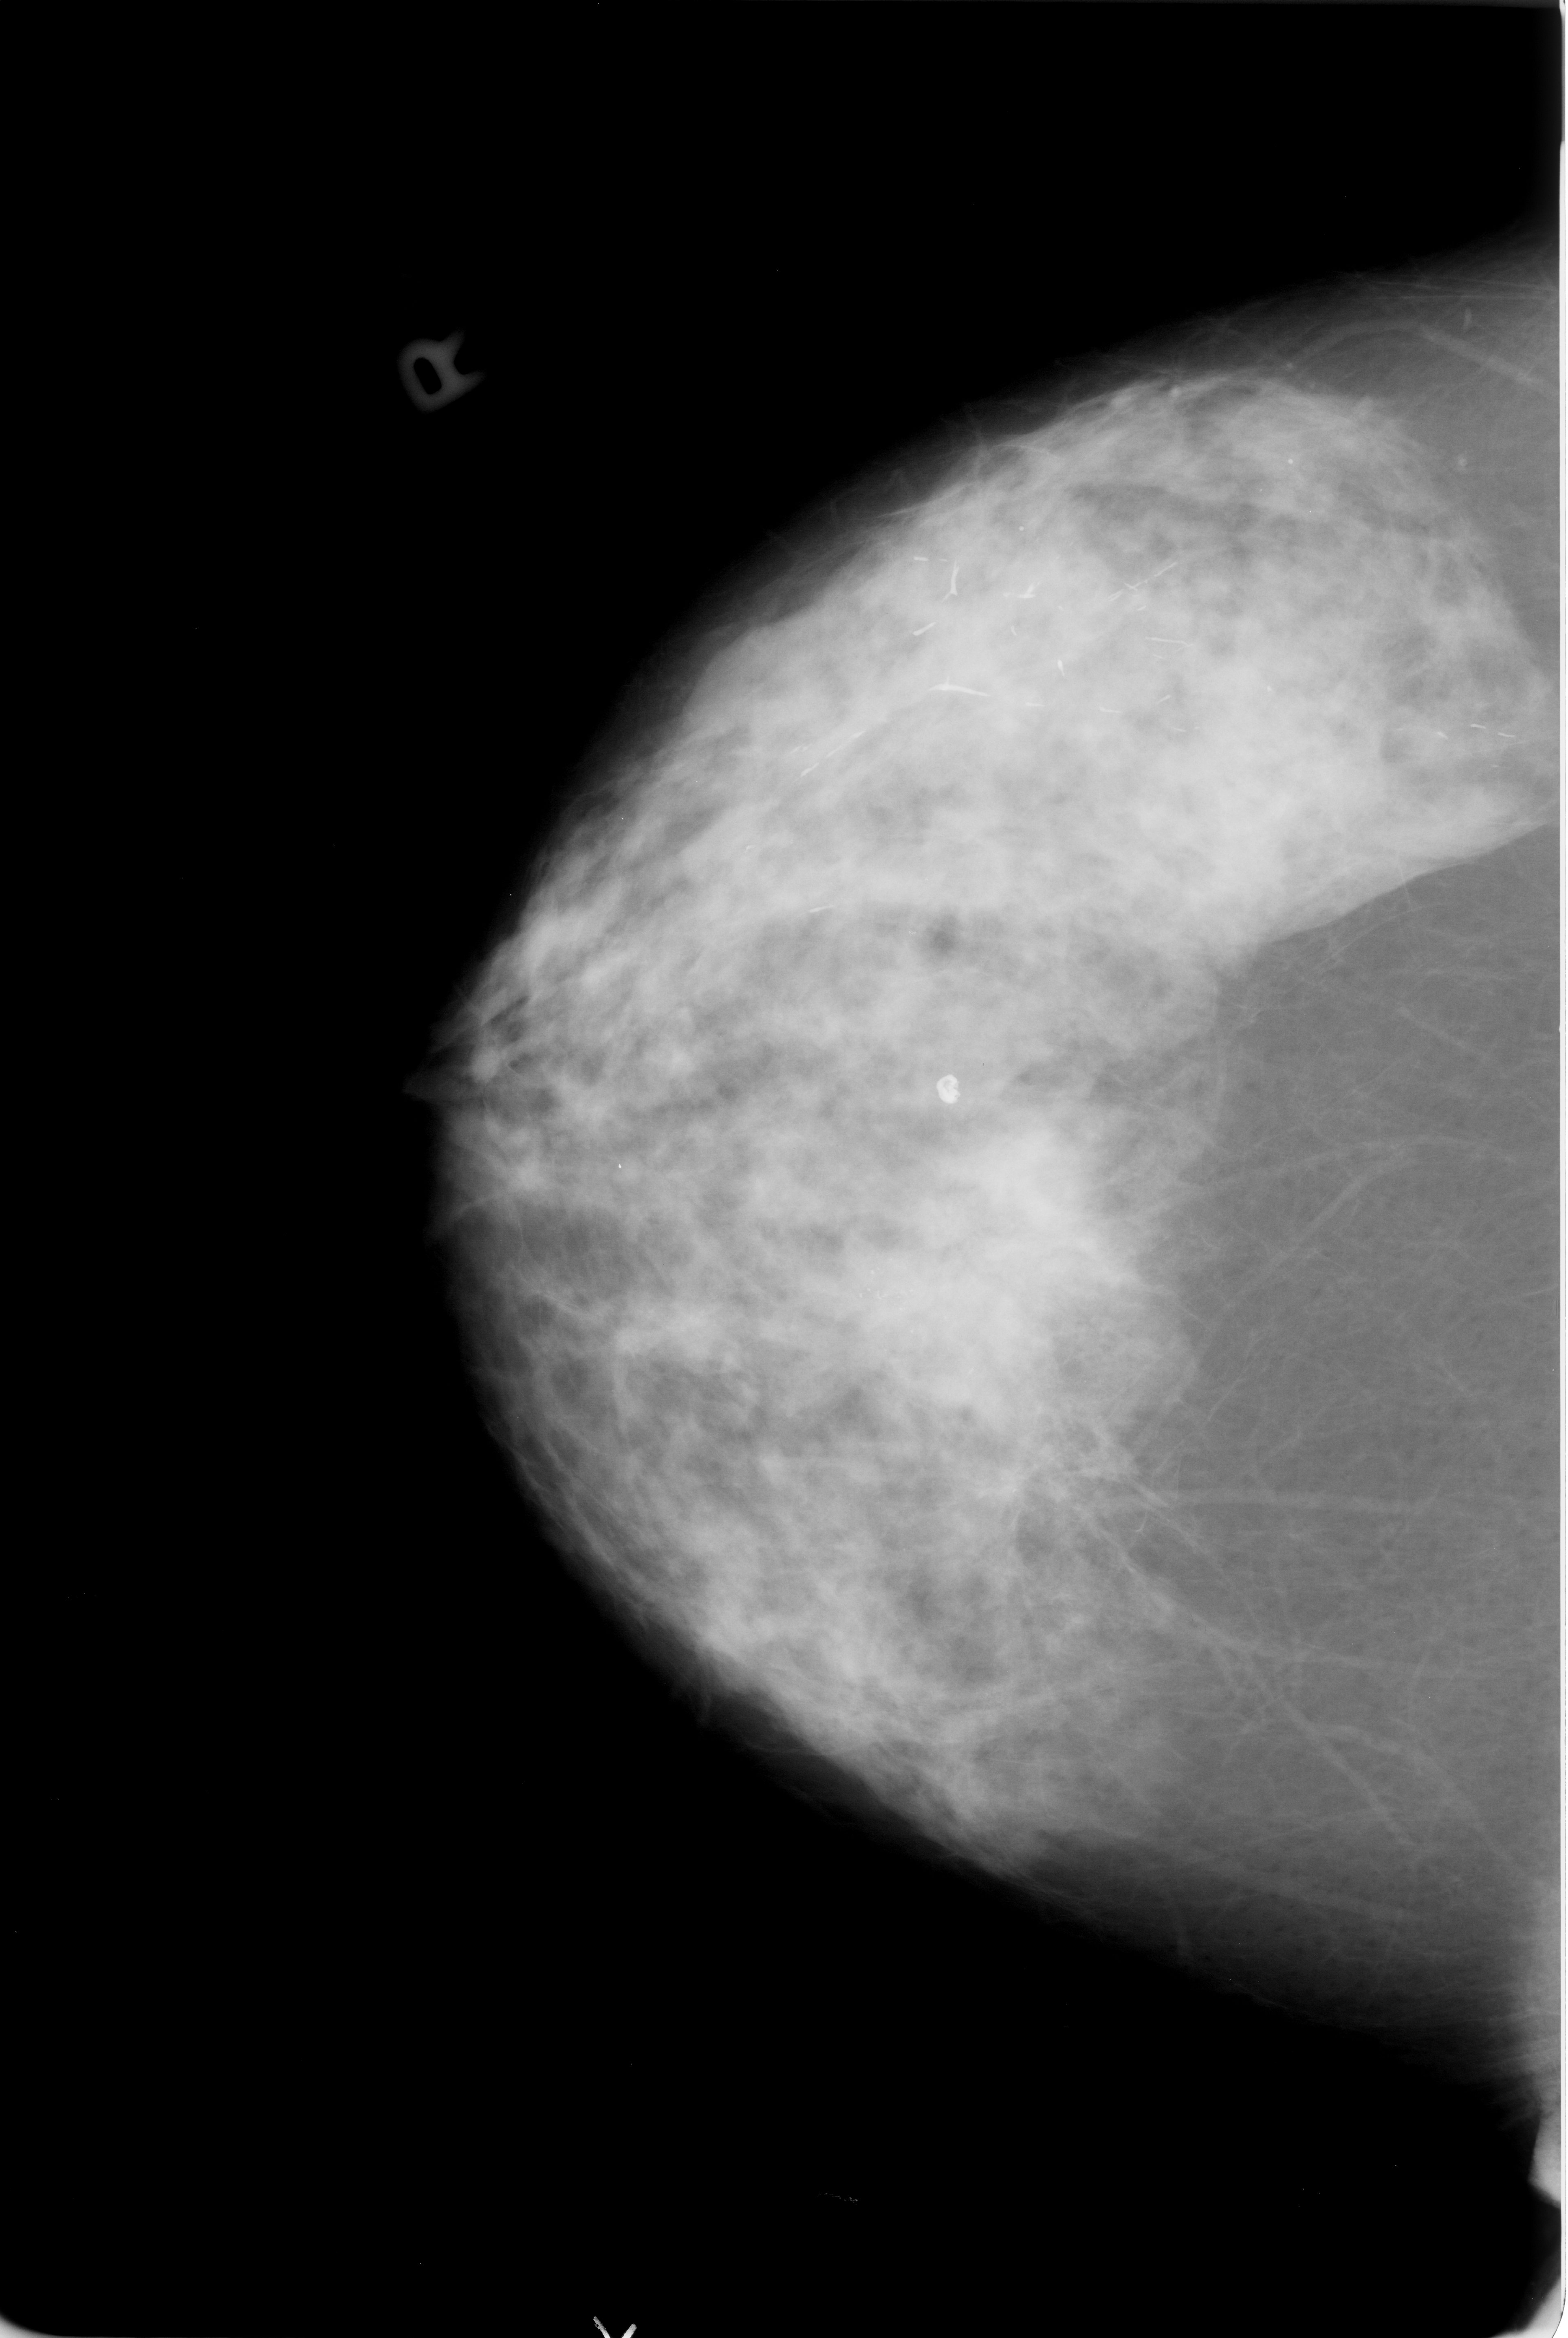
Digitized screen-film mammogram. Right breast. CC view. BI-RADS breast density category 3 (scale 1–4). 1568 × 2338 image matrix.
Marked abnormalities (boxes around the expert regions of interest):
- Finding 1 of 3: calcifications, morphology pleomorphic, distribution clustered; BI-RADS assessment category 4; pathology (as recorded): malignant: box from (x=883, y=1274) to (x=904, y=1305) px
- Finding 2 of 3: calcifications, morphology pleomorphic, distribution clustered; BI-RADS assessment category 4; pathology result (as recorded, not read from the image): malignant: (x=919, y=1274)–(x=950, y=1305)
- Finding 3 of 3: calcifications, morphology pleomorphic, distribution clustered; BI-RADS assessment category 4; pathology result (as recorded, not read from the image): malignant: (x=925, y=1330)–(x=953, y=1367)